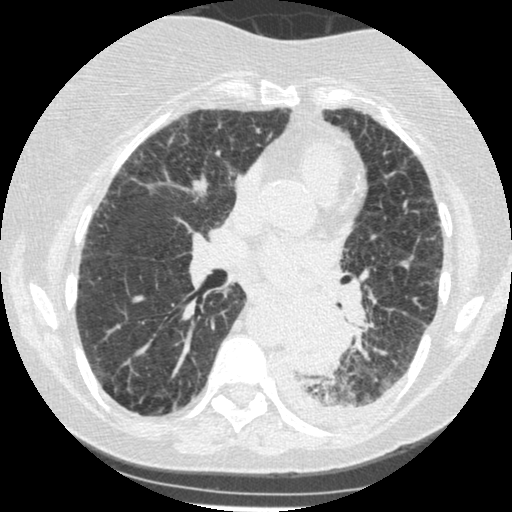
Low-dose screening chest CT, axial slice; third annual screen; lung window (W 1500 / L -600 HU). Female, age 60 years at enrolment. Former smoker at enrolment.
Lesion marked by an expert reader, bounding box [x1, y1, x2, y2] px = [273, 305, 342, 374]. Screening reader's record for this exam (one nodule recorded; not confirmed to be the boxed lesion): non-calcified nodule or mass ≥4 mm, left lower lobe, 54 × 38 mm, smooth margins, soft tissue attenuation, pre-existing on the prior screen: yes; interval growth: yes. Lung cancer was diagnosed 15 days after this screen: small cell carcinoma, NOS, left lower lobe, undifferentiated (G4), stage IV (AJCC 6th edition), 69 mm at pathology.